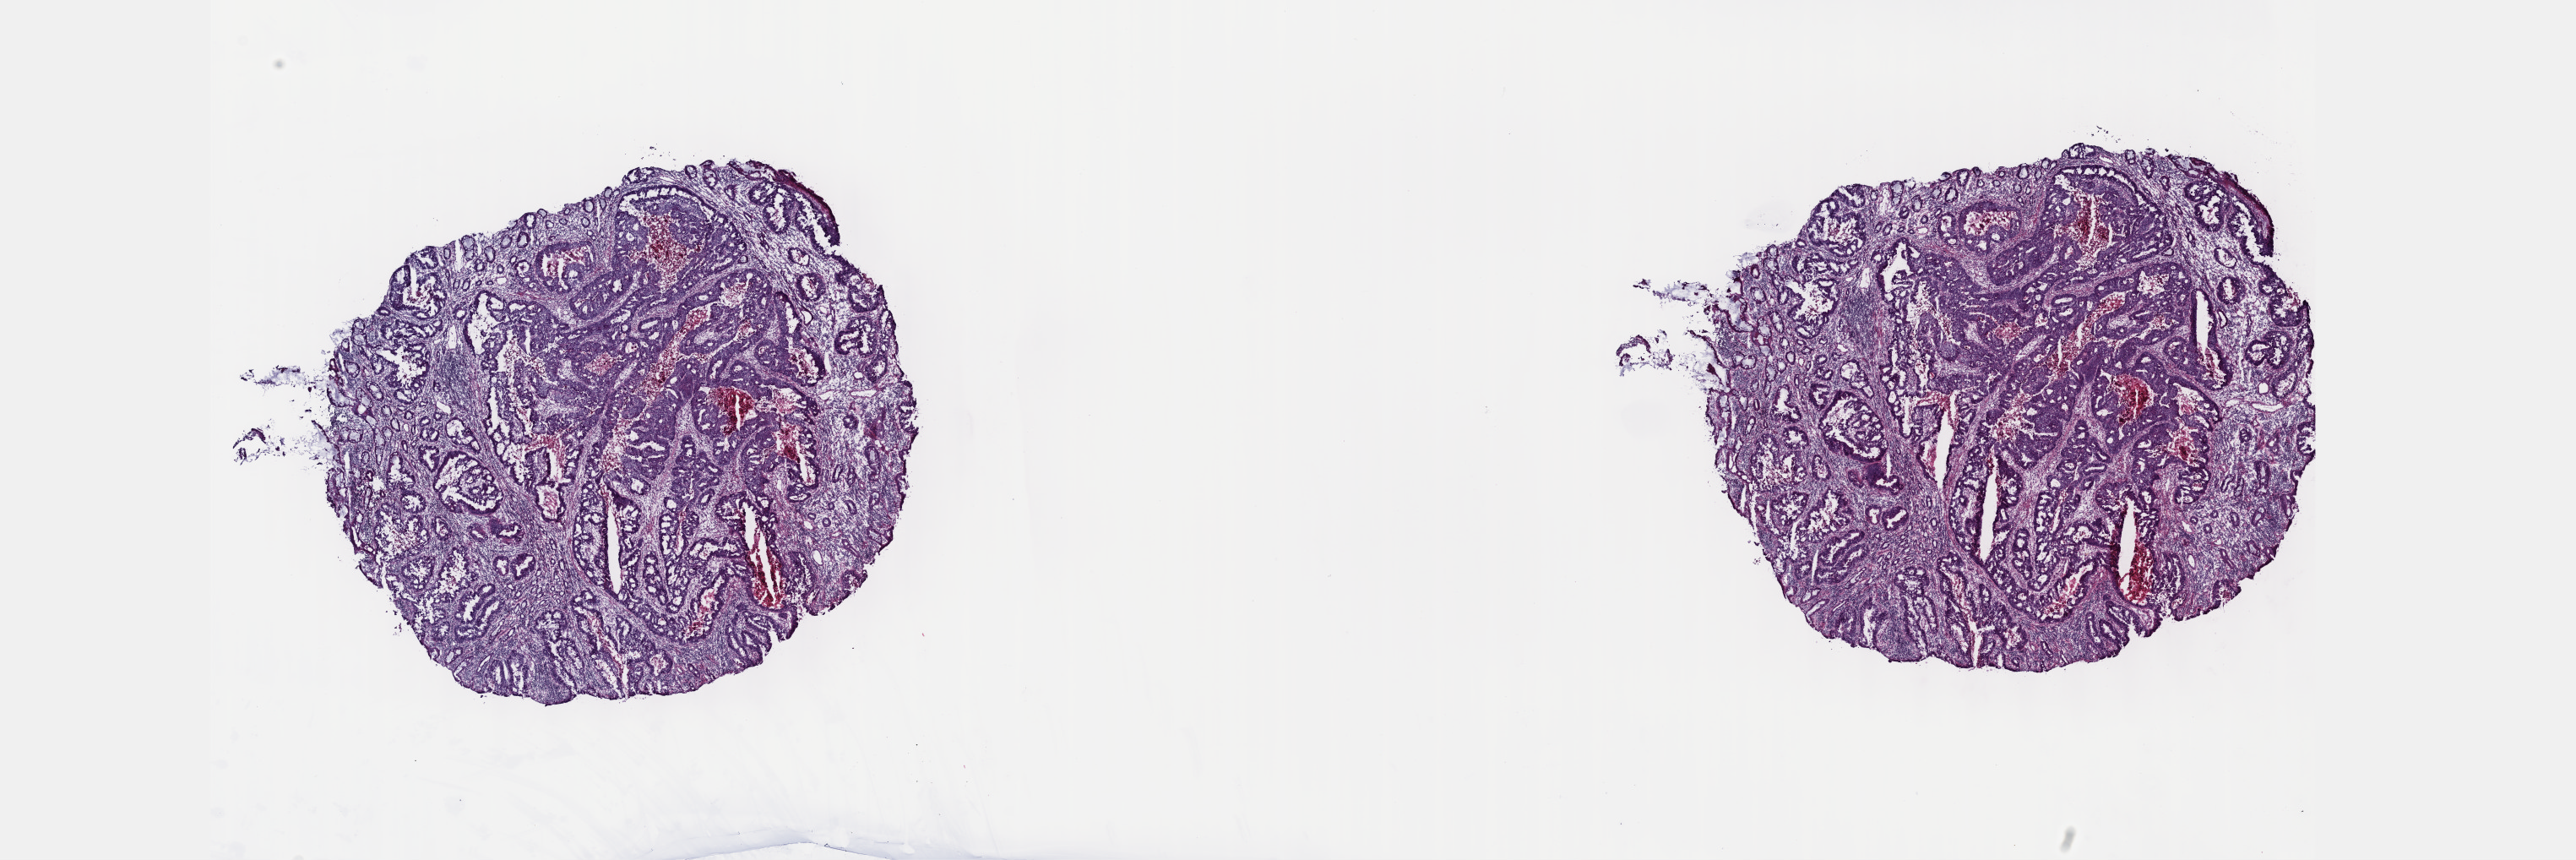
Whole-slide histology image, Hematoxylin and eosin (H&E) stained — shown as a low-resolution overview of the whole scanned area (about 24.6 x 8.2 mm), frozen section, sample: primary tumour, colon. Male, age 82 years at initial diagnosis. Pathologist review of this section (percent, as recorded): tumour cells 60%, tumour nuclei 65%, normal cells 5%, stromal cells 30%, necrosis 5%. Inflammatory infiltration, as recorded: lymphocyte infiltration 10%, monocyte infiltration 0%, neutrophil infiltration 0%.
Pathologic diagnosis: Adenocarcinoma, NOS (sigmoid colon). AJCC pathologic stage: IIA (7th edition).